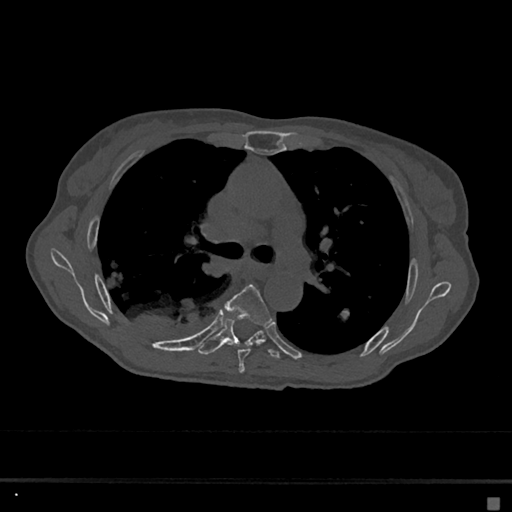
CT including the spine, one axial slice. Position 442 of 797 along the scan axis. Bone window (W 1800 / L 400 HU). 512 × 512 image matrix, field of view 360 × 360 mm. Female patient, age 68 years. Case-level facts recorded for this patient, not image findings: primary cancer: renal.
Structures marked on this image (semi-automatically segmented with operator editing):
- T5 vertebra: box from (x=225, y=284) to (x=272, y=374) px
- T6 vertebra: (x=197, y=319)–(x=280, y=359)